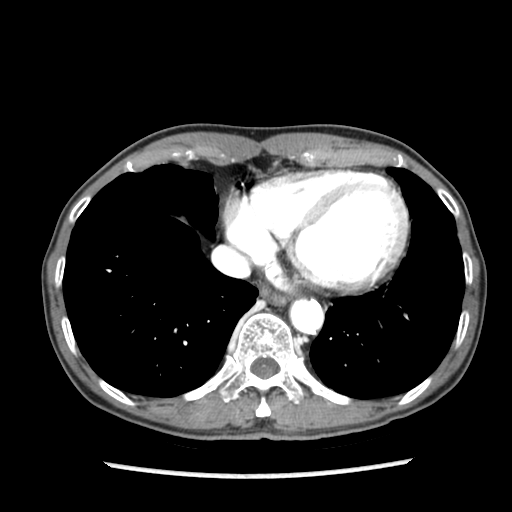
Contrast-enhanced abdominal CT (liver protocol), one axial slice. Slice 78 of 87 in the series (ordered by position). Soft-tissue window (W 400 / L 40 HU). 2.5 mm slice thickness. 512 × 512 image matrix, field of view 300 × 300 mm. From the clinical record (not read from this slice): diagnosis: hepatocellular carcinoma (patient treated with transarterial chemoembolisation; whether this scan precedes or follows treatment is not stated here); TNM stage (as recorded): Stage-IIIB; Child-Pugh class: A; tumour differentiation: well differentiated.
Annotated regions visible in this slice (semi-automatic segmentation, software-assisted and operator-edited):
- abdominal aorta: bounding box (x1, y1, x2, y2) in pixels: (291, 301, 321, 333)